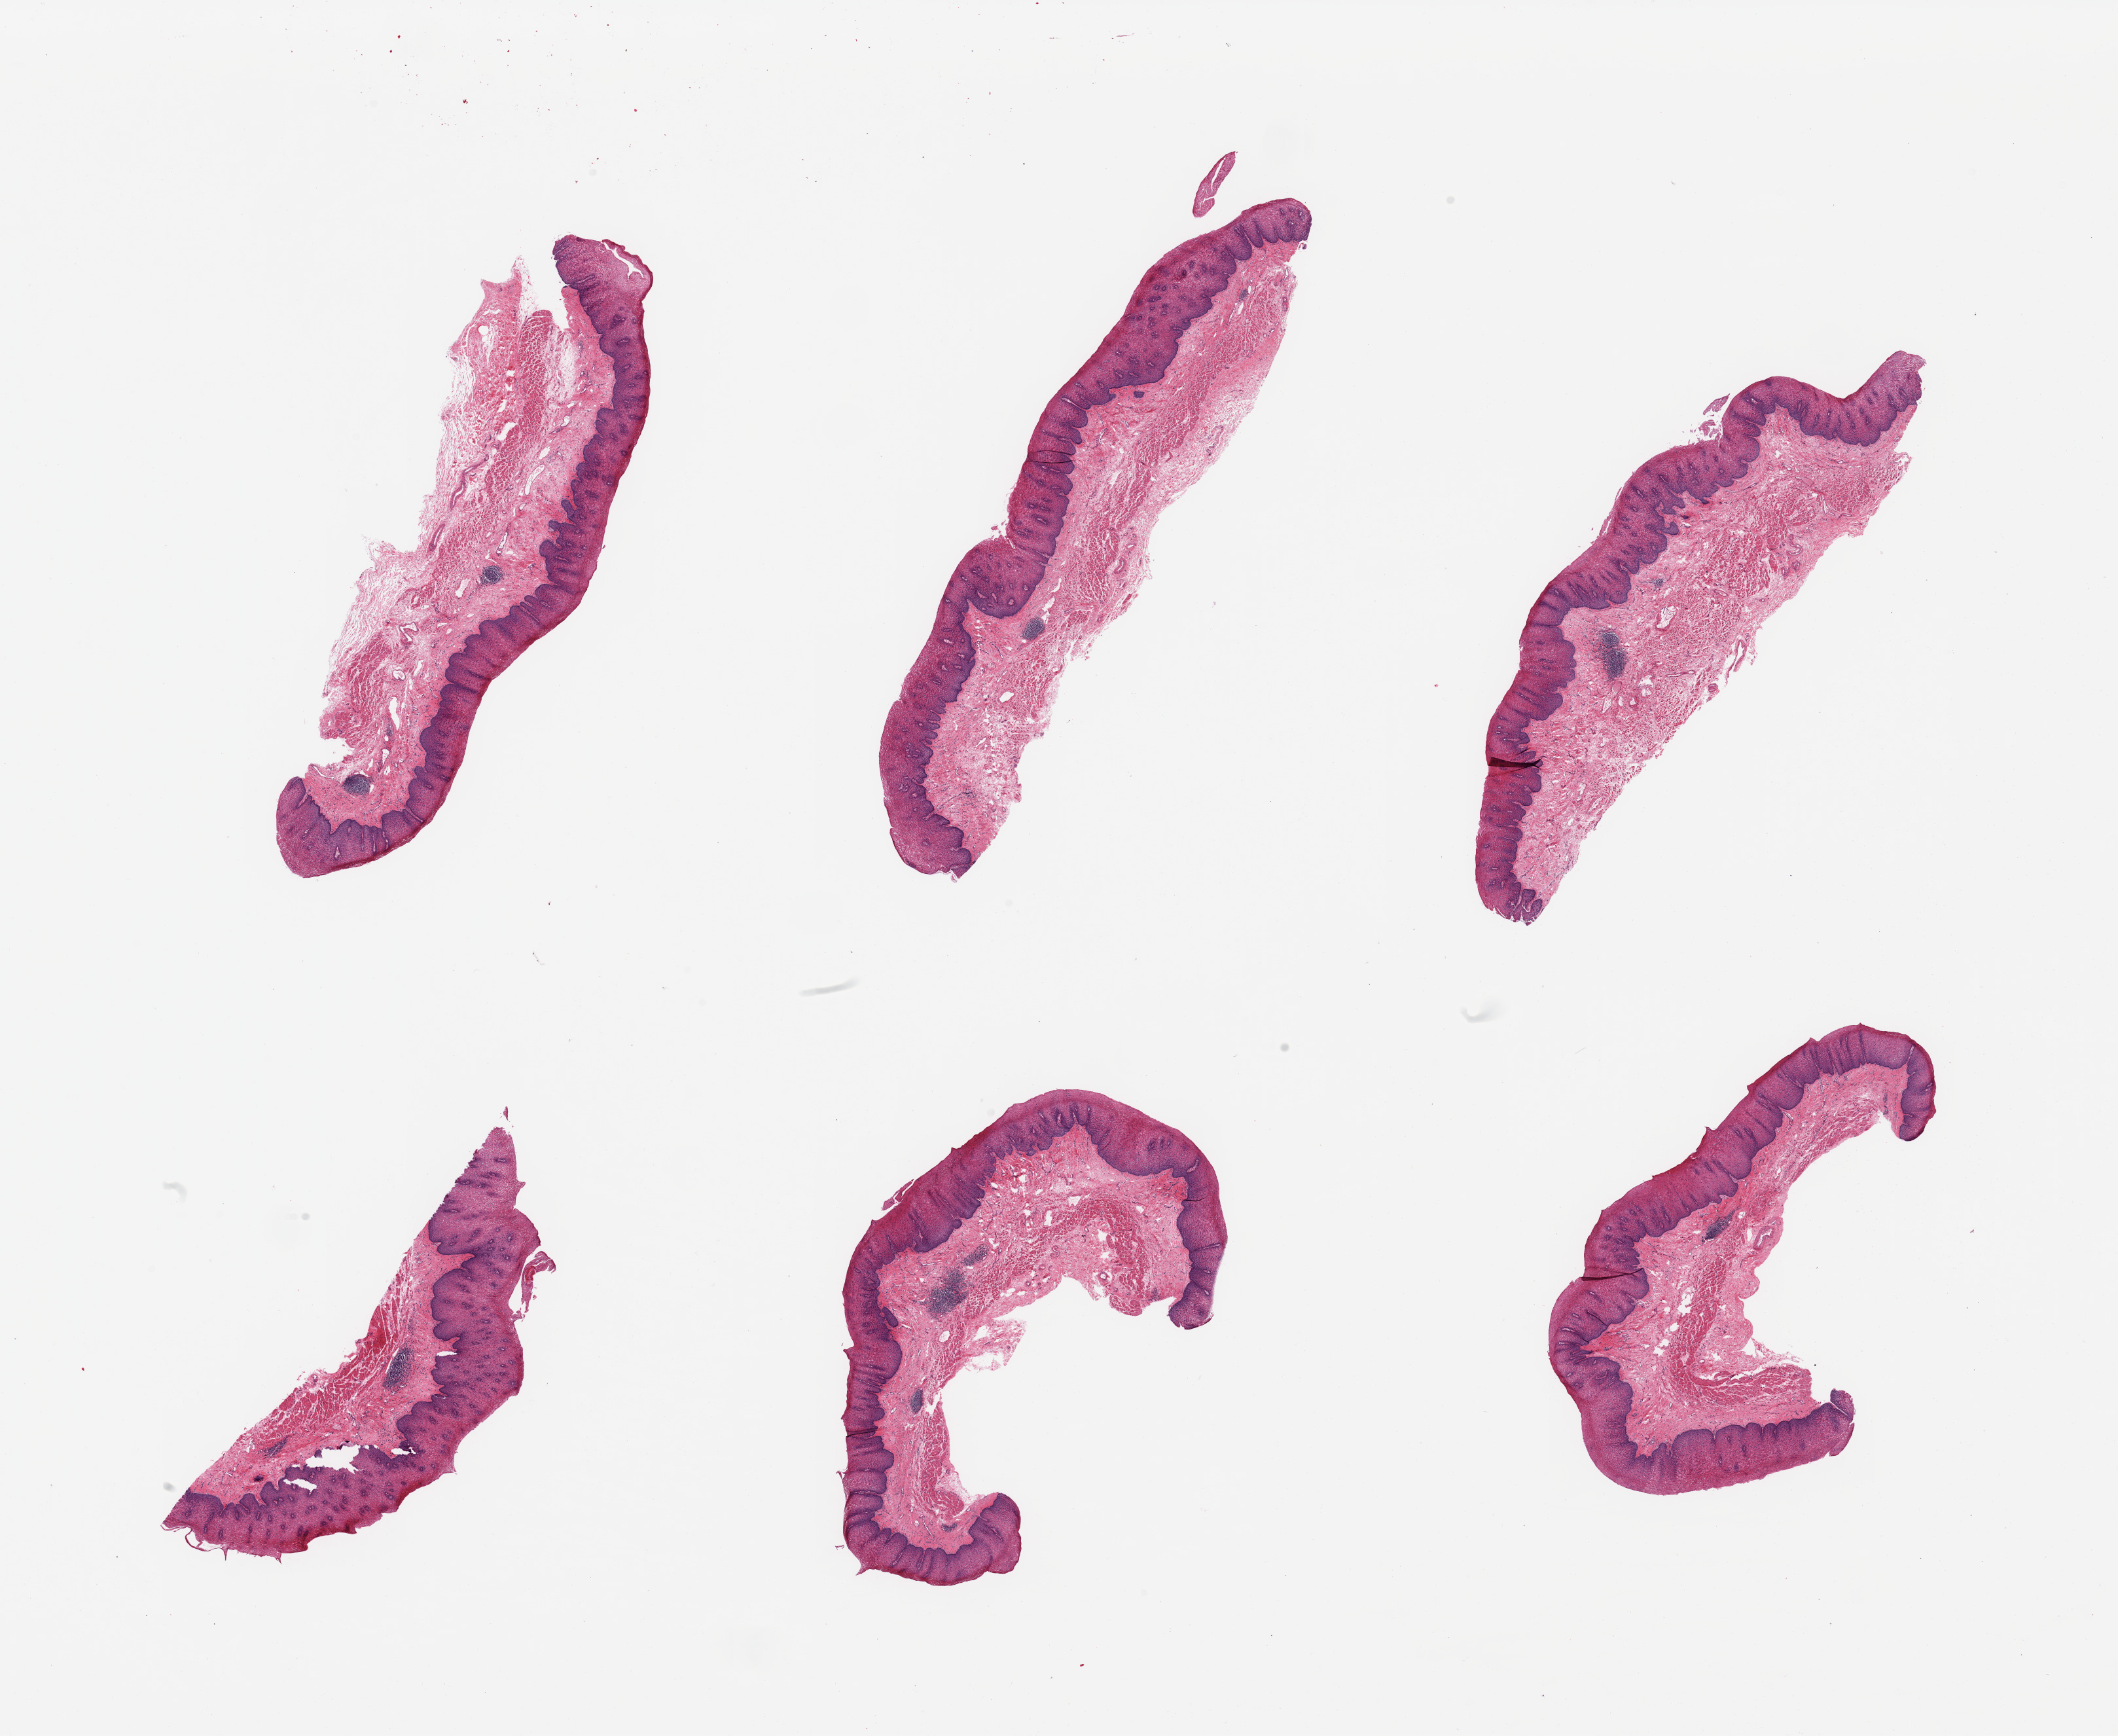
Whole-slide image, H&E stain, brightfield — low-resolution overview of the scanned area, about 25.6 x 21.0 mm; PAXgene-fixed, paraffin-embedded tissue; sampled site (target tissue): esophageal mucous membrane; tissue donor sample. Male donor.
* review note (as recorded): 6 pieces, squamous mucosa up to ~0.6mm, ~20-30% thickness